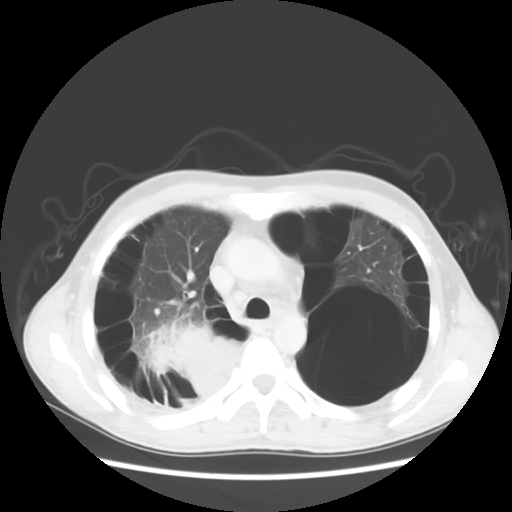
Chest CT, one axial slice; reconstruction kernel STANDARD; 140 kVp; lung window (W 1500 / L -600 HU); 5 mm slice thickness; 512 × 512 image matrix, field of view 351 × 351 mm. Male patient, age 41 years. From the clinical record (not read from this slice): clinical TNM (as recorded): T4 N0 M1a; histopathological grade: G3.
Outlined on this slice (bounding box drawn by a radiologist):
- lung tumour (recorded histology: large cell carcinoma): bounding box <134,315,246,406> (left, top, right, bottom; pixels)